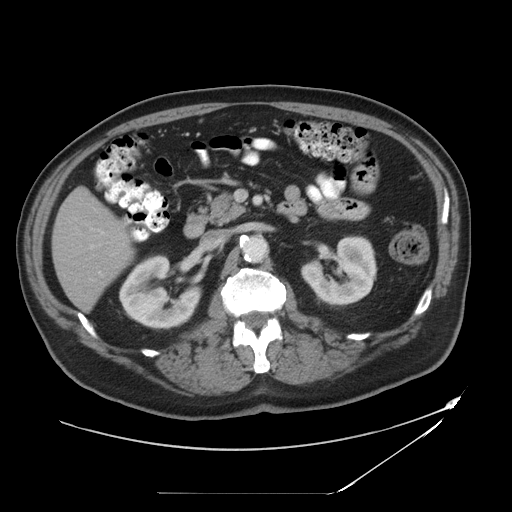
Contrast-enhanced abdominal CT, one axial slice. Position 19 of 49 along the scan axis. Reconstruction kernel STANDARD. Soft-tissue window (W 400 / L 40 HU). 5 mm slice thickness. 512 × 512 image matrix, field of view 461 × 461 mm. Male patient, age 72 years. From the clinical record (not read from this slice): diagnosis: colorectal cancer liver metastases, imaged before liver resection; multiple liver metastases: no.
Outlined on this slice (manually delineated by an expert):
- hepatic veins: bounding box (x1, y1, x2, y2) in pixels: (88, 243, 102, 250)
- liver: (54, 191, 132, 309)
- planned liver remnant (the part of the liver to remain after resection): (54, 191, 132, 309)
- portal vein (with intrahepatic branches): (98, 230, 104, 275)